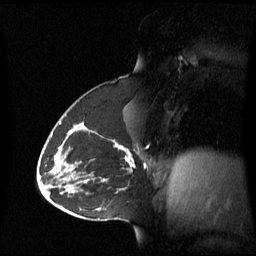
Breast MRI (dynamic contrast-enhanced), one sagittal slice; position 36 of 60 along the scan axis; dynamic contrast-enhanced series, image 2 of 3 at this slice position (ordered by acquisition); 1.5 T; TE 4.2 ms, TR 8.4 ms; 2.8 mm slice thickness; 256 × 256 image matrix, field of view 270 × 270 mm. Patient: female, 43 years. From the clinical record (not read from this slice): setting: breast cancer imaged before/during neoadjuvant chemotherapy; receptor status: triple-negative.
Annotated regions visible in this slice (semi-automatically segmented with operator editing):
- analysis volume of interest (the breast-tissue region the enhancement analysis was run in; not a lesion): box from (x=62, y=124) to (x=137, y=180) px
- tumour enhancement mask (voxels above the 70 % enhancement threshold inside the analysis volume of interest): (x=113, y=140)–(x=134, y=168)